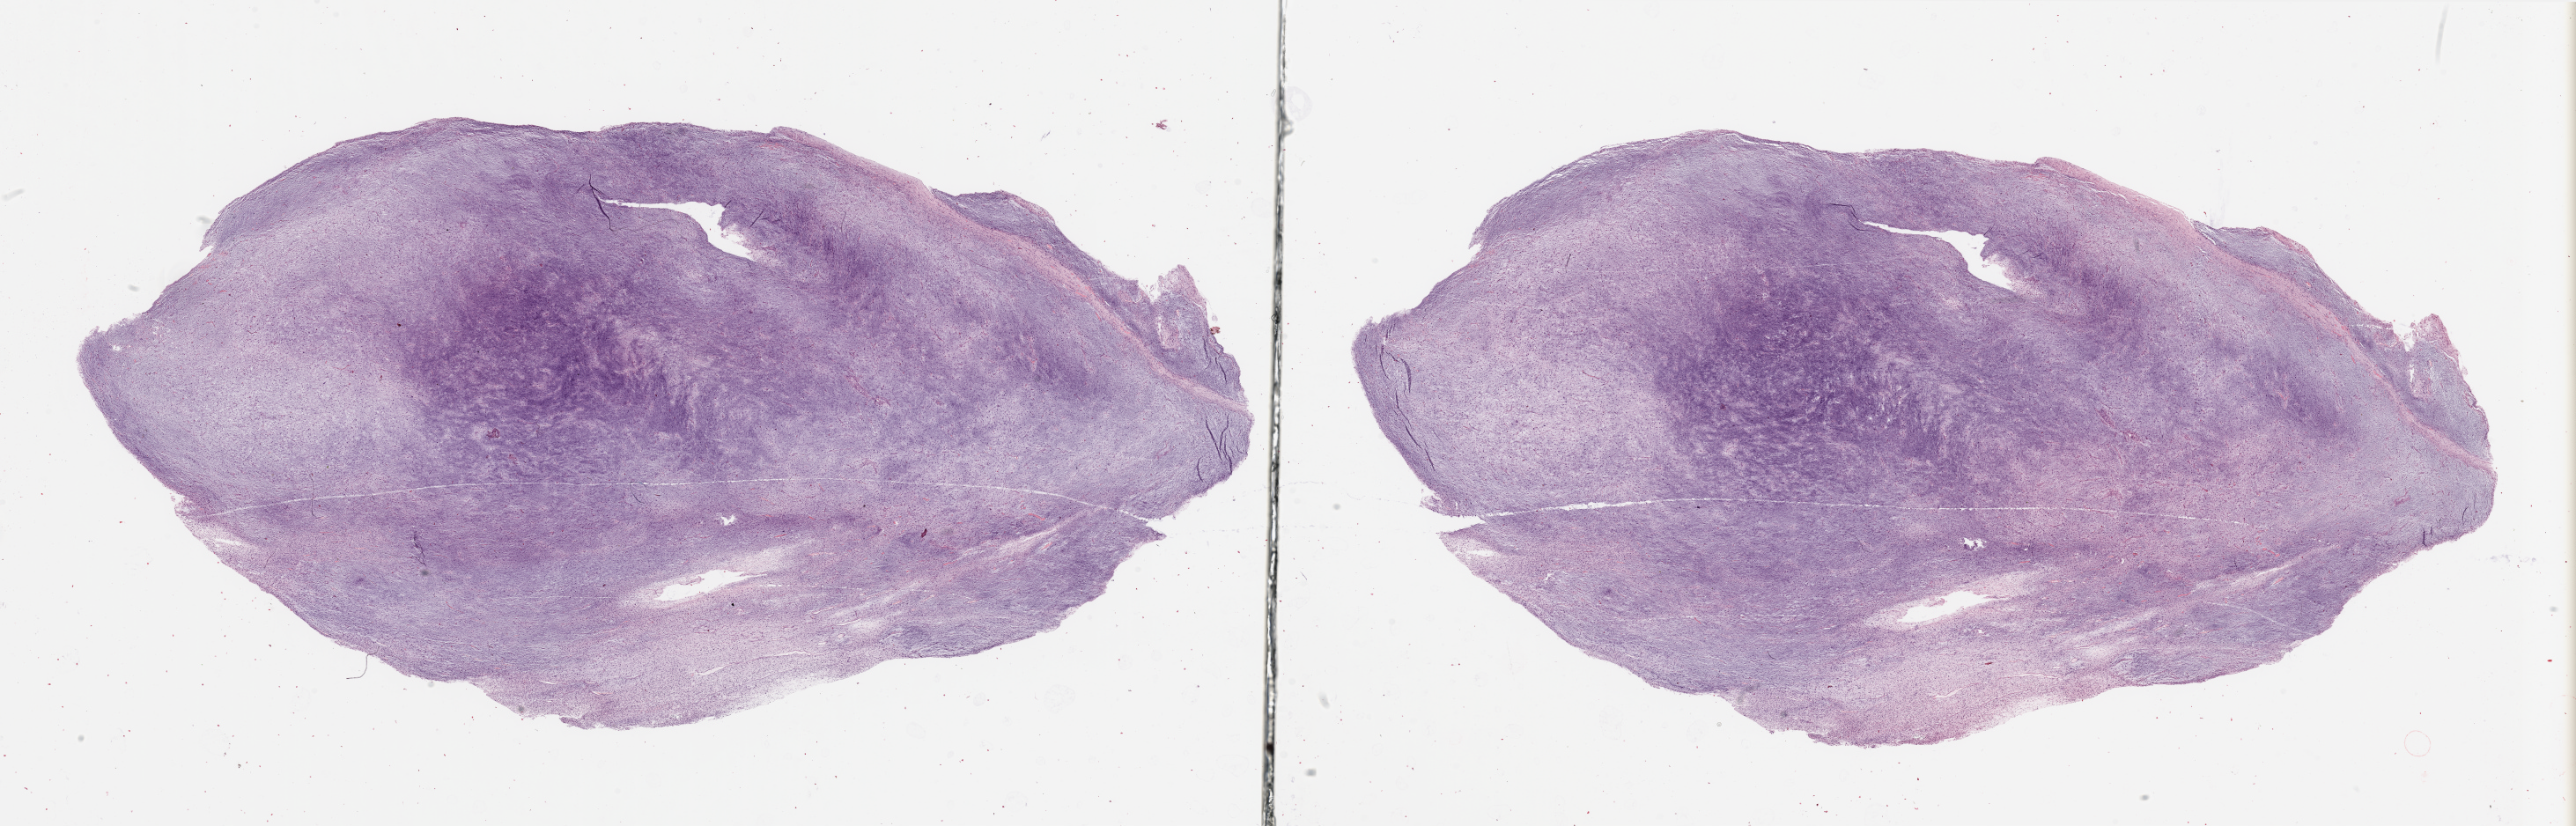
Whole-slide histology image, Hematoxylin and eosin (H&E) stained — whole scanned area (about 46.3 x 14.8 mm) shown as a low-resolution overview; tumour tissue sample. 70-year-old male patient.
Patient diagnosis (cohort enrolment): sarcoma (site not recorded at cohort level). Primary tumour site (as recorded): lower extremity.